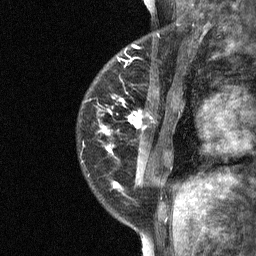
Breast MRI (dynamic contrast-enhanced), one sagittal slice. Position 18 of 64 along the scan axis. Dynamic contrast-enhanced study with each time point stored as its own series, time point 2 of 3 at this slice position (early post-contrast, ordered by acquisition time). 1.5 T. TE 4.8 ms, TR 27 ms. 256 × 256 image matrix, field of view 180 × 180 mm. Female patient, age 34 years. From the clinical record (not read from this slice): setting: breast cancer imaged before/during neoadjuvant chemotherapy; receptor status: HR-positive, HER2-negative.
Annotated regions visible in this slice (semi-automatically segmented with operator editing):
- analysis volume of interest (the breast-tissue region the enhancement analysis was run in; not a lesion): bounding box <78,44,181,191> (left, top, right, bottom; pixels)
- tumour enhancement mask (voxels above the 90 % enhancement threshold inside the analysis volume of interest): <100,59,143,188>